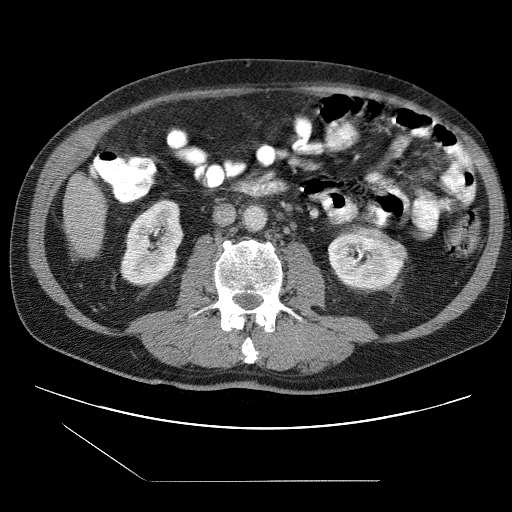
Contrast-enhanced abdominal CT (liver protocol), one axial slice; position 13 of 109 along the scan axis; 120 kVp; one of 2 acquisitions stored at this slice position; soft-tissue window (W 400 / L 40 HU); 2.5 mm slice thickness; 512 × 512 image matrix, field of view 400 × 400 mm. From the clinical record (not read from this slice): diagnosis: hepatocellular carcinoma (patient treated with transarterial chemoembolisation; whether this scan precedes or follows treatment is not stated here); TNM stage (as recorded): Stage-IIIB.
Outlined on this slice (semi-automatic segmentation, software-assisted and operator-edited):
- liver parenchyma outside the tumour (the mass and vessels are separate outlines, so this box may not span the whole liver): bounding box <64,176,106,257> (left, top, right, bottom; pixels)